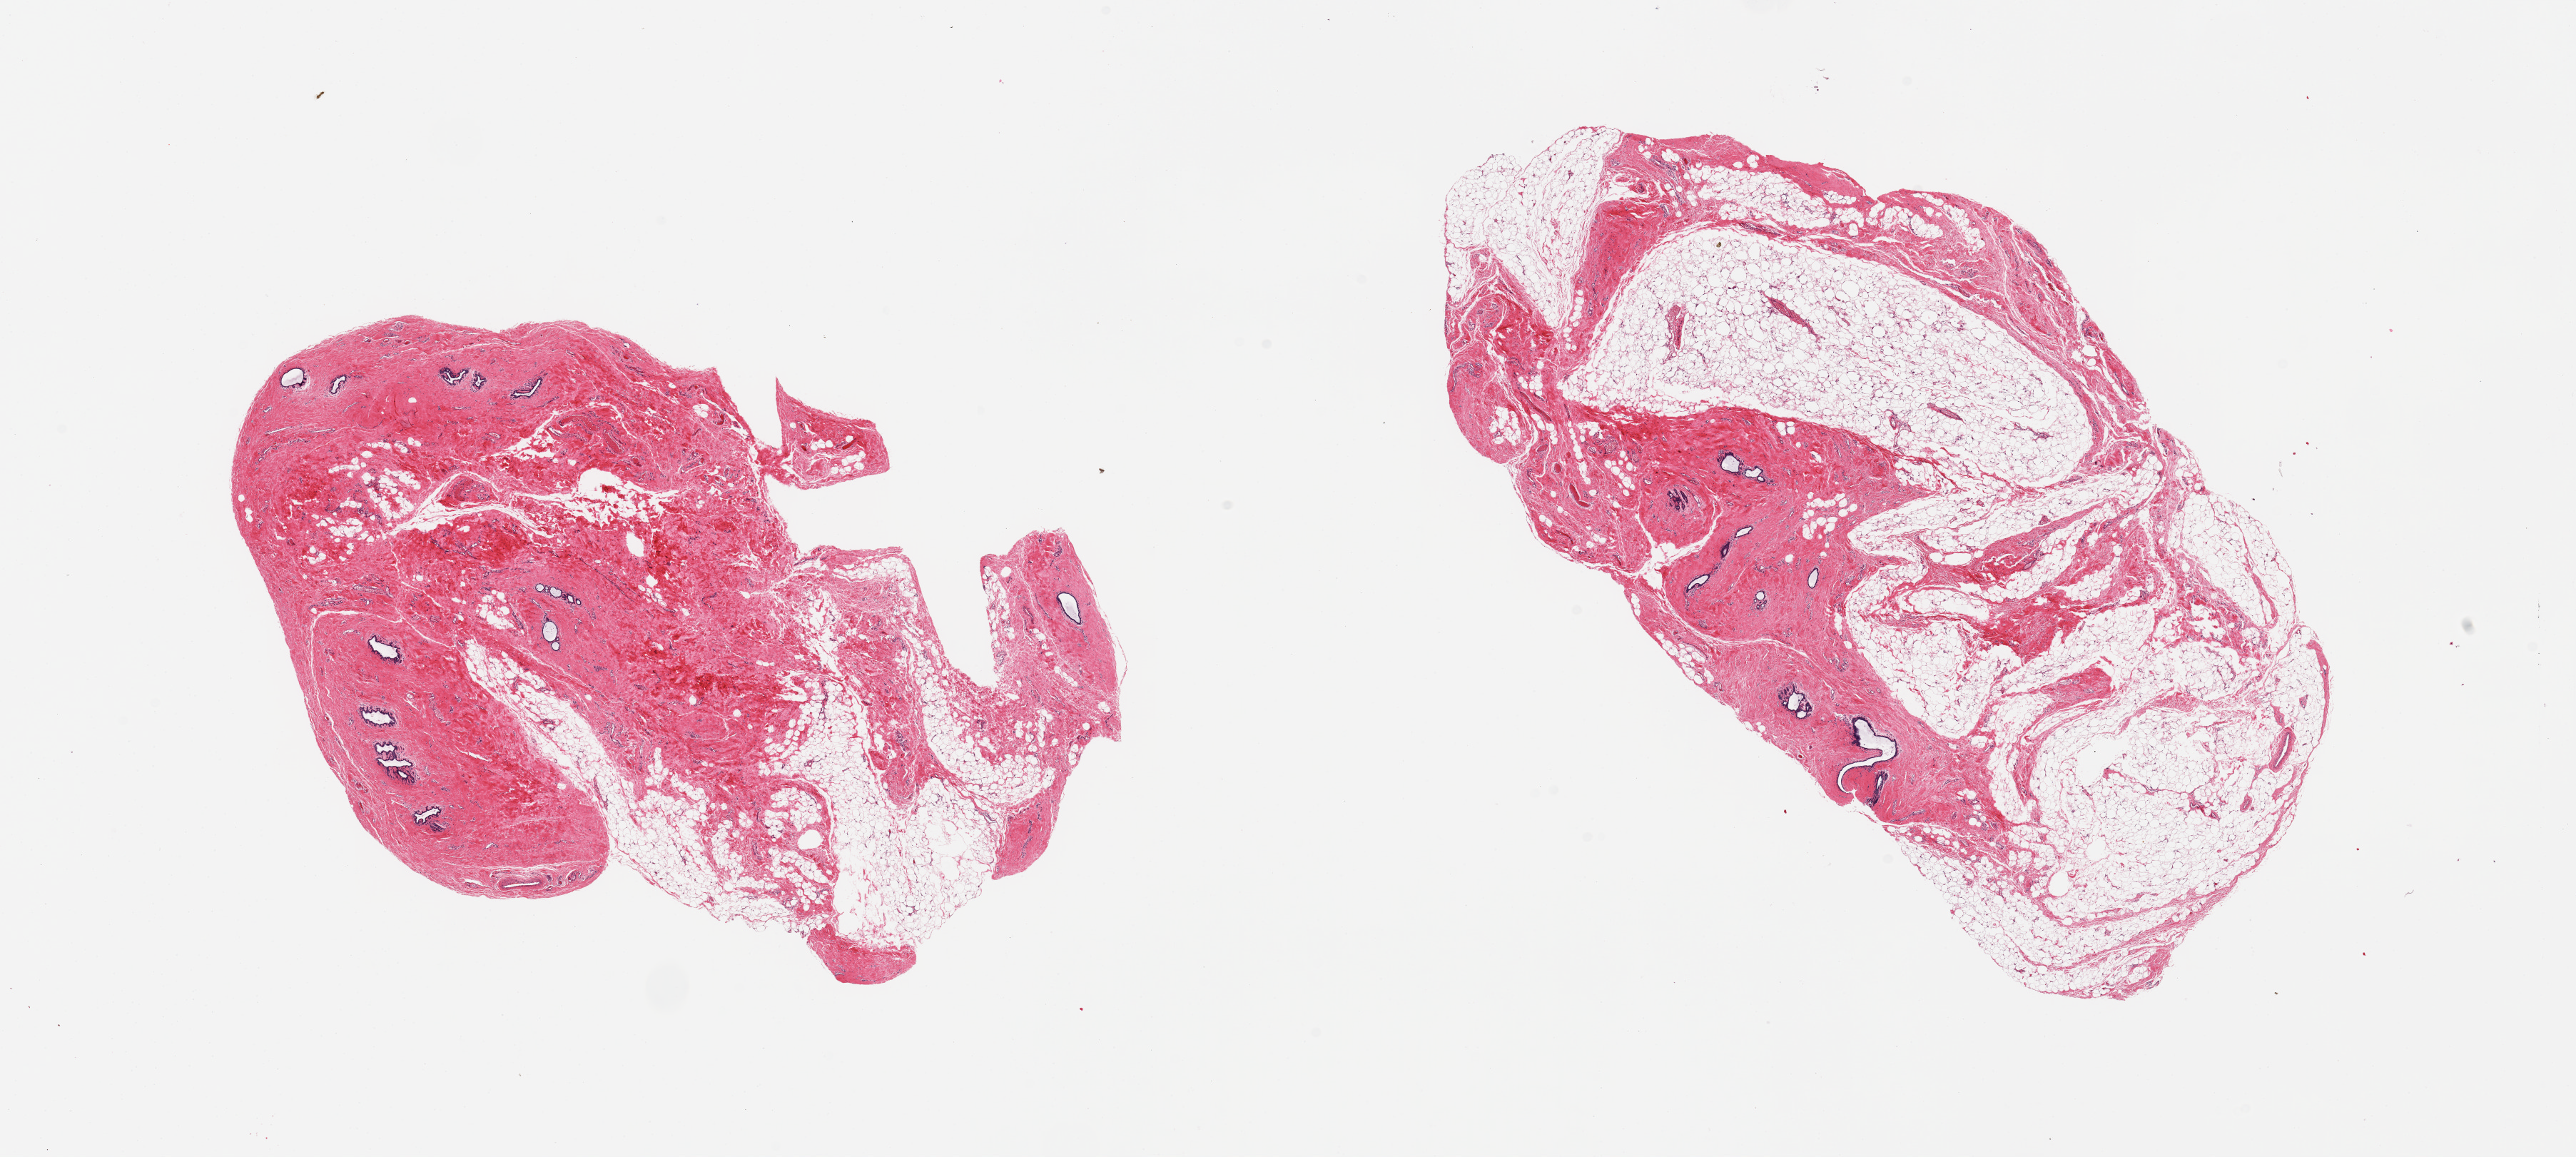
Digitized hematoxylin and eosin (H&E)-stained section — shown as a low-resolution overview of the whole scanned area (about 28.5 x 12.8 mm); PAXgene-fixed paraffin-embedded (PFPE) section; sampled site (target tissue): breast; tissue donor sample.
* reviewer comment on this tissue sample: 2 pieces; ~20 and 60% fat, remainder is fibrous tissue and ducts with mild gynecomastoid change